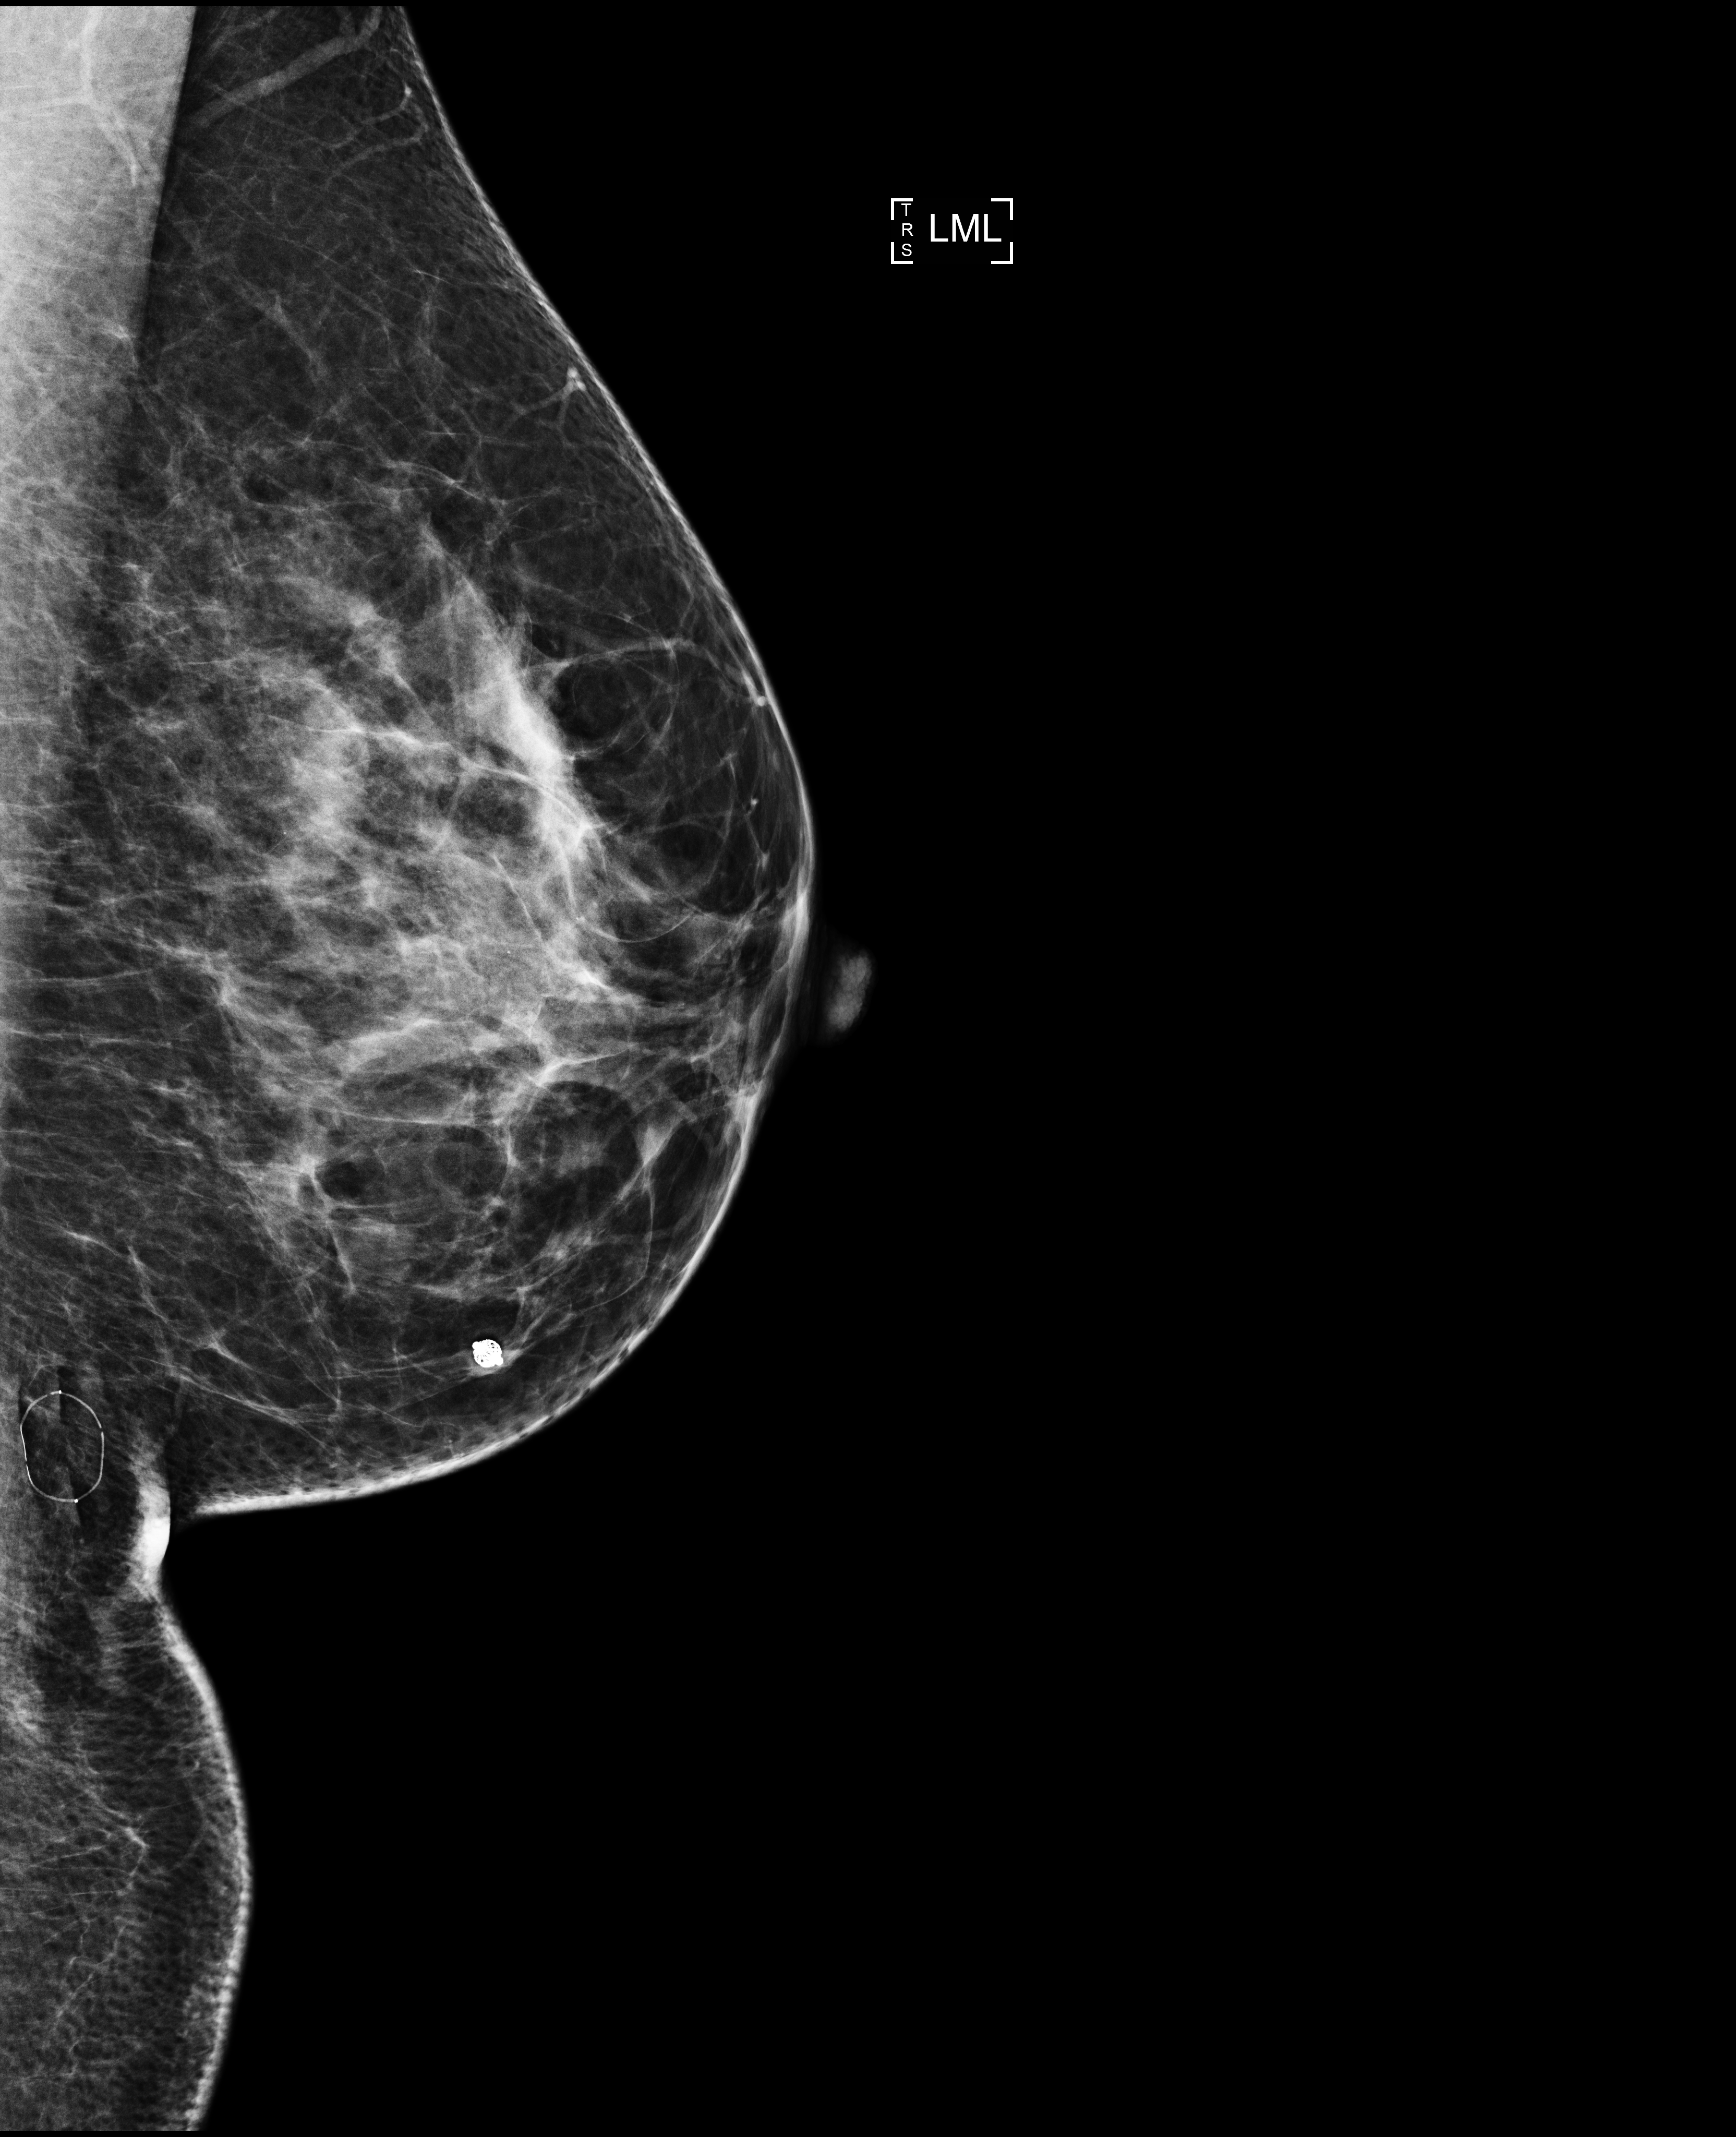
Annual screening mammography examination; compressed breast thickness 58 mm; system: Selenia Dimensions. Female patient, age 42 years.
Image type: full-field digital mammogram. Breast: left. Projection: mediolateral (ML) view.